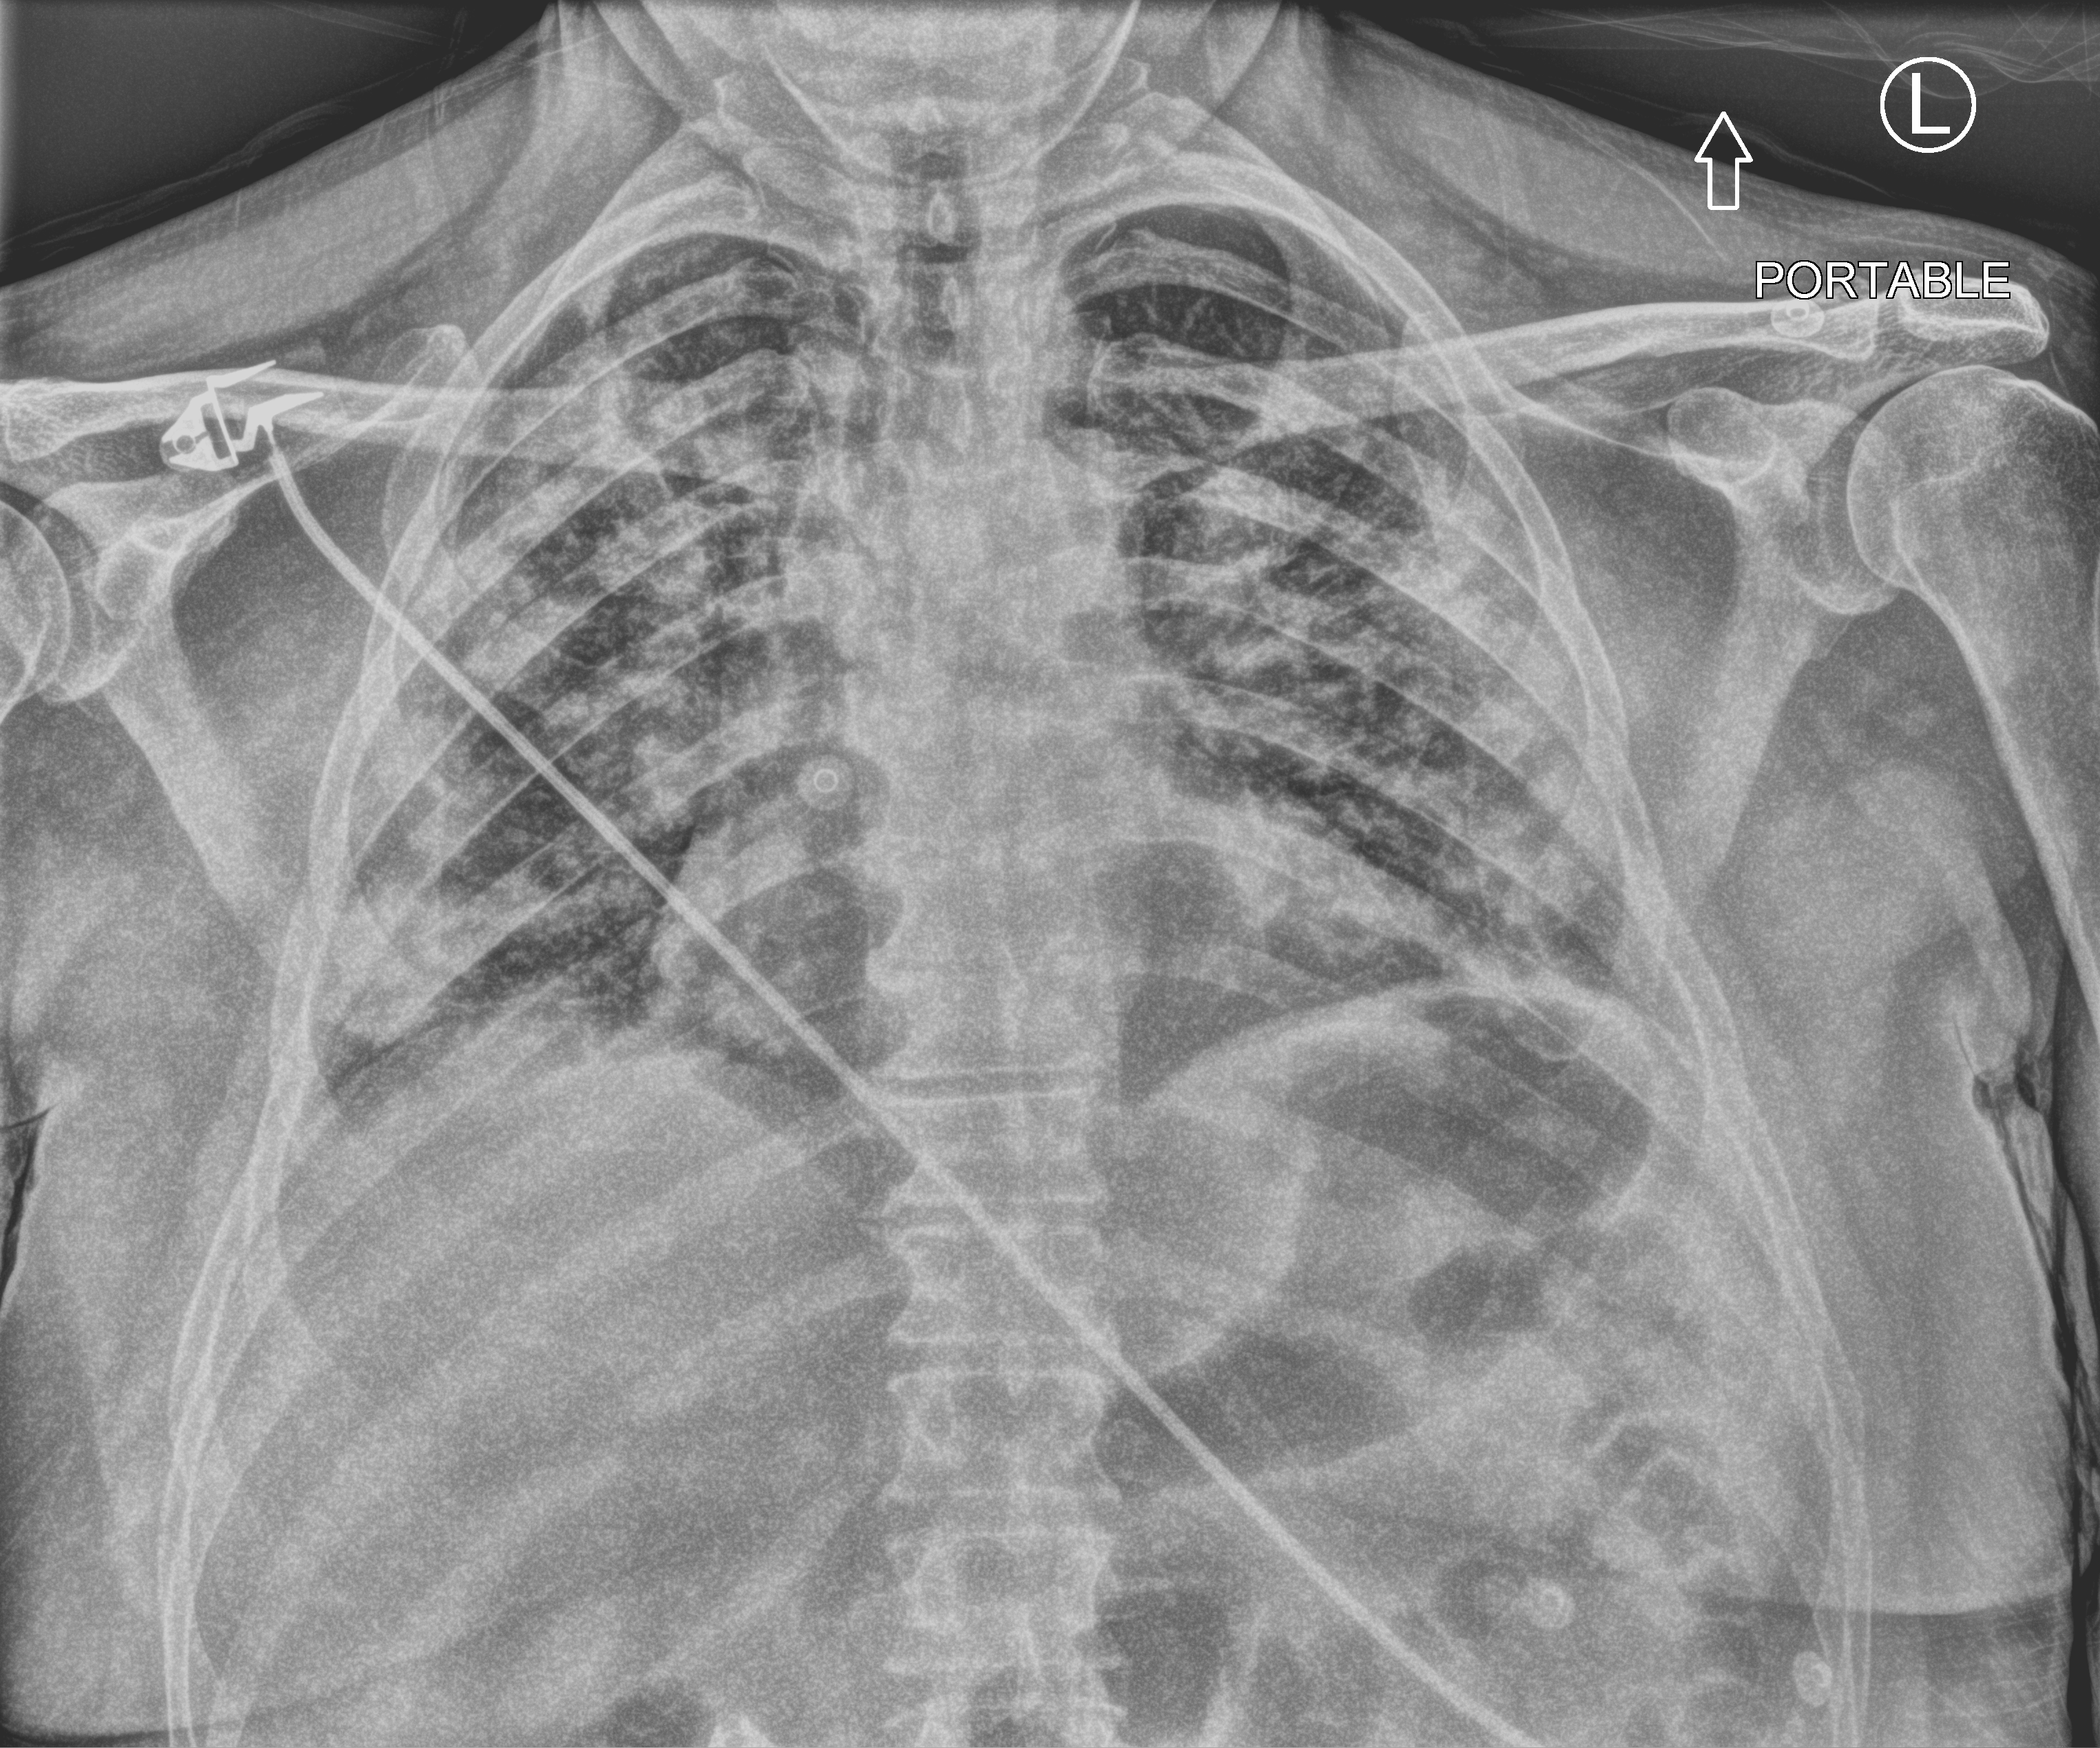
Chest X-ray (portable). Male patient hospitalised with COVID-19, age 18–59 years.
Hospital-stay facts (about this admission, not read from this image; timing relative to this image not recorded): chronic kidney disease (admission record): no; length of hospital stay: 12 days; mechanically ventilated during this hospital stay: no.